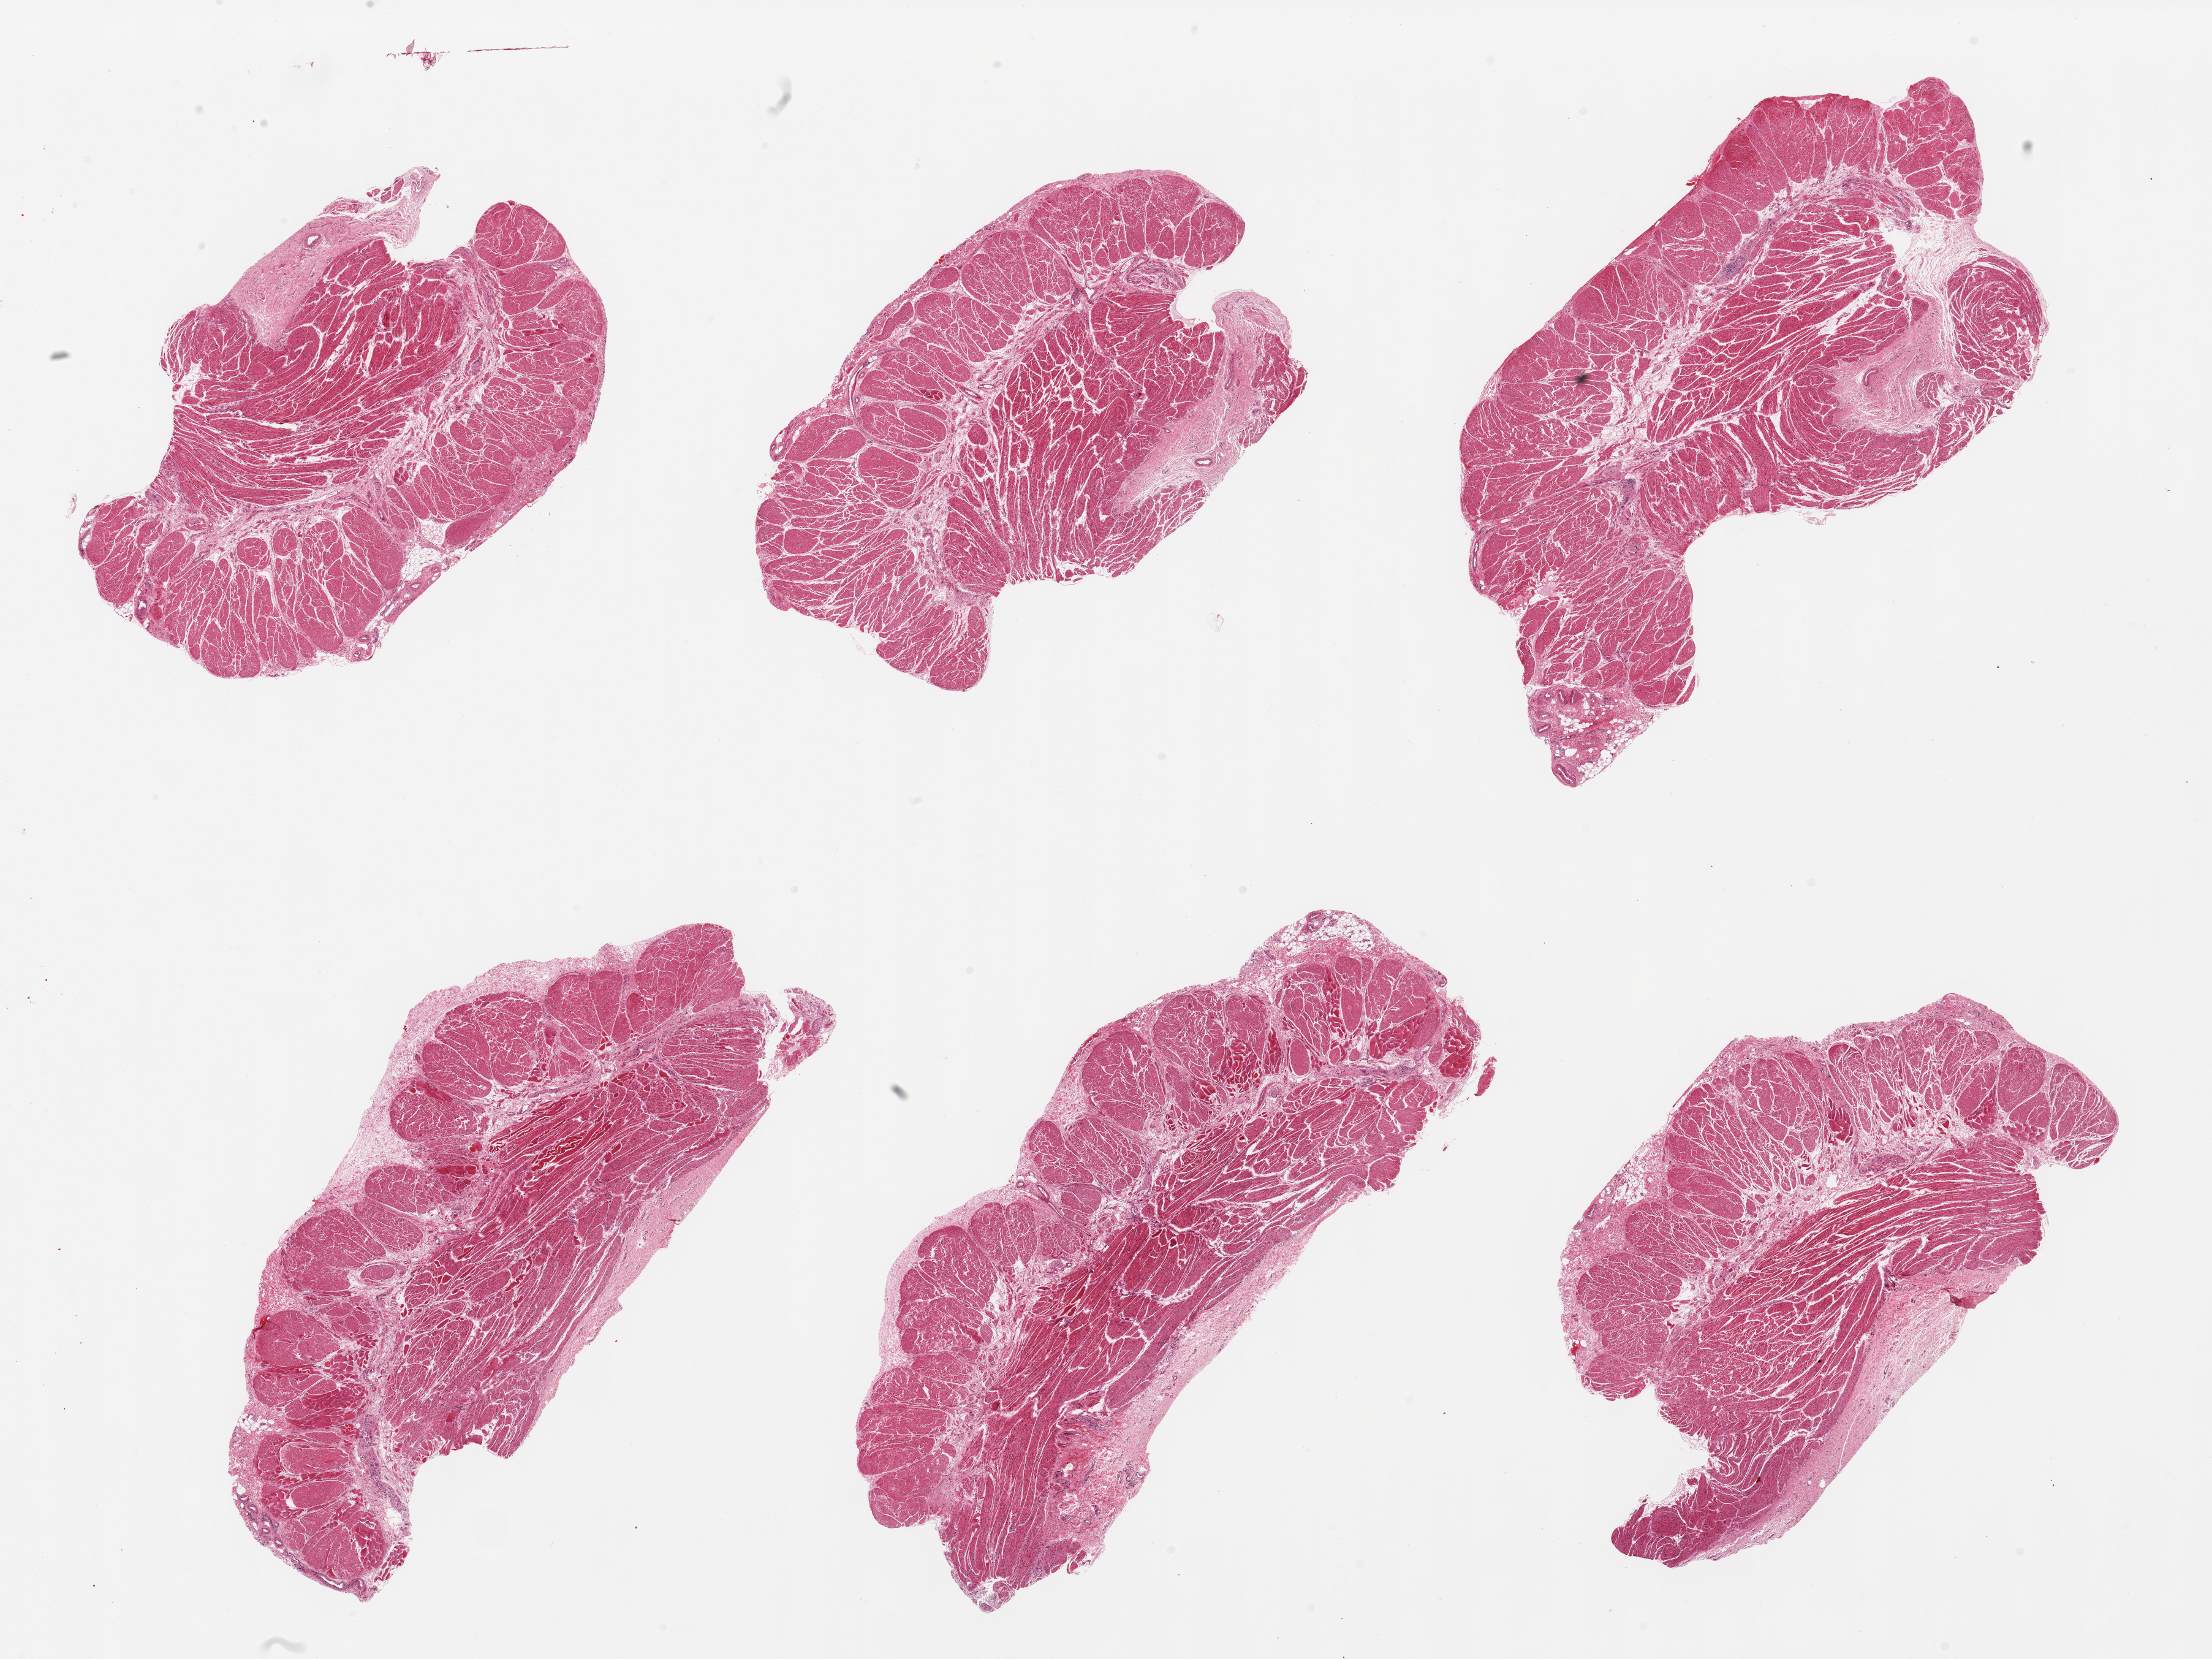
Whole-slide image, hematoxylin and eosin (H&E) stain — shown as a low-resolution overview of the whole scanned area (about 28.5 x 21.4 mm); PAXgene-fixed, paraffin-embedded tissue; target tissue: esophageal muscle; tissue donor sample. Donor sex: female.
Reviewer comment on this tissue sample: 6 pieces, confirmed target muscularis.